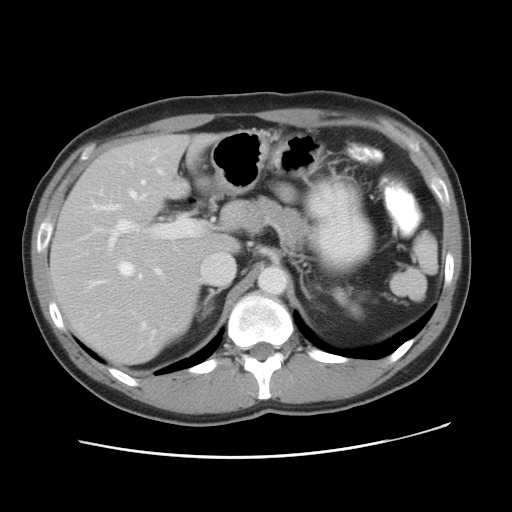
Contrast-enhanced abdominal CT, one axial slice; slice 31 of 49 in the series (ordered by position); 120 kVp; intravenous contrast given; soft-tissue window (W 400 / L 40 HU); 512 × 512 image matrix. Male patient, age 41 years. Case-level facts recorded for this patient, not image findings: diagnosis: colorectal cancer liver metastases, imaged before liver resection; multiple liver metastases: yes; largest metastasis: 0.7 cm; disease in both lobes: yes.
Annotated regions visible in this slice (manually delineated by an expert):
- hepatic veins: bounding box [x1, y1, x2, y2] px = [91, 156, 234, 287]
- liver: [52, 135, 239, 364]
- planned liver remnant (the part of the liver to remain after resection): [102, 135, 238, 252]
- portal vein (with intrahepatic branches): [109, 217, 198, 328]